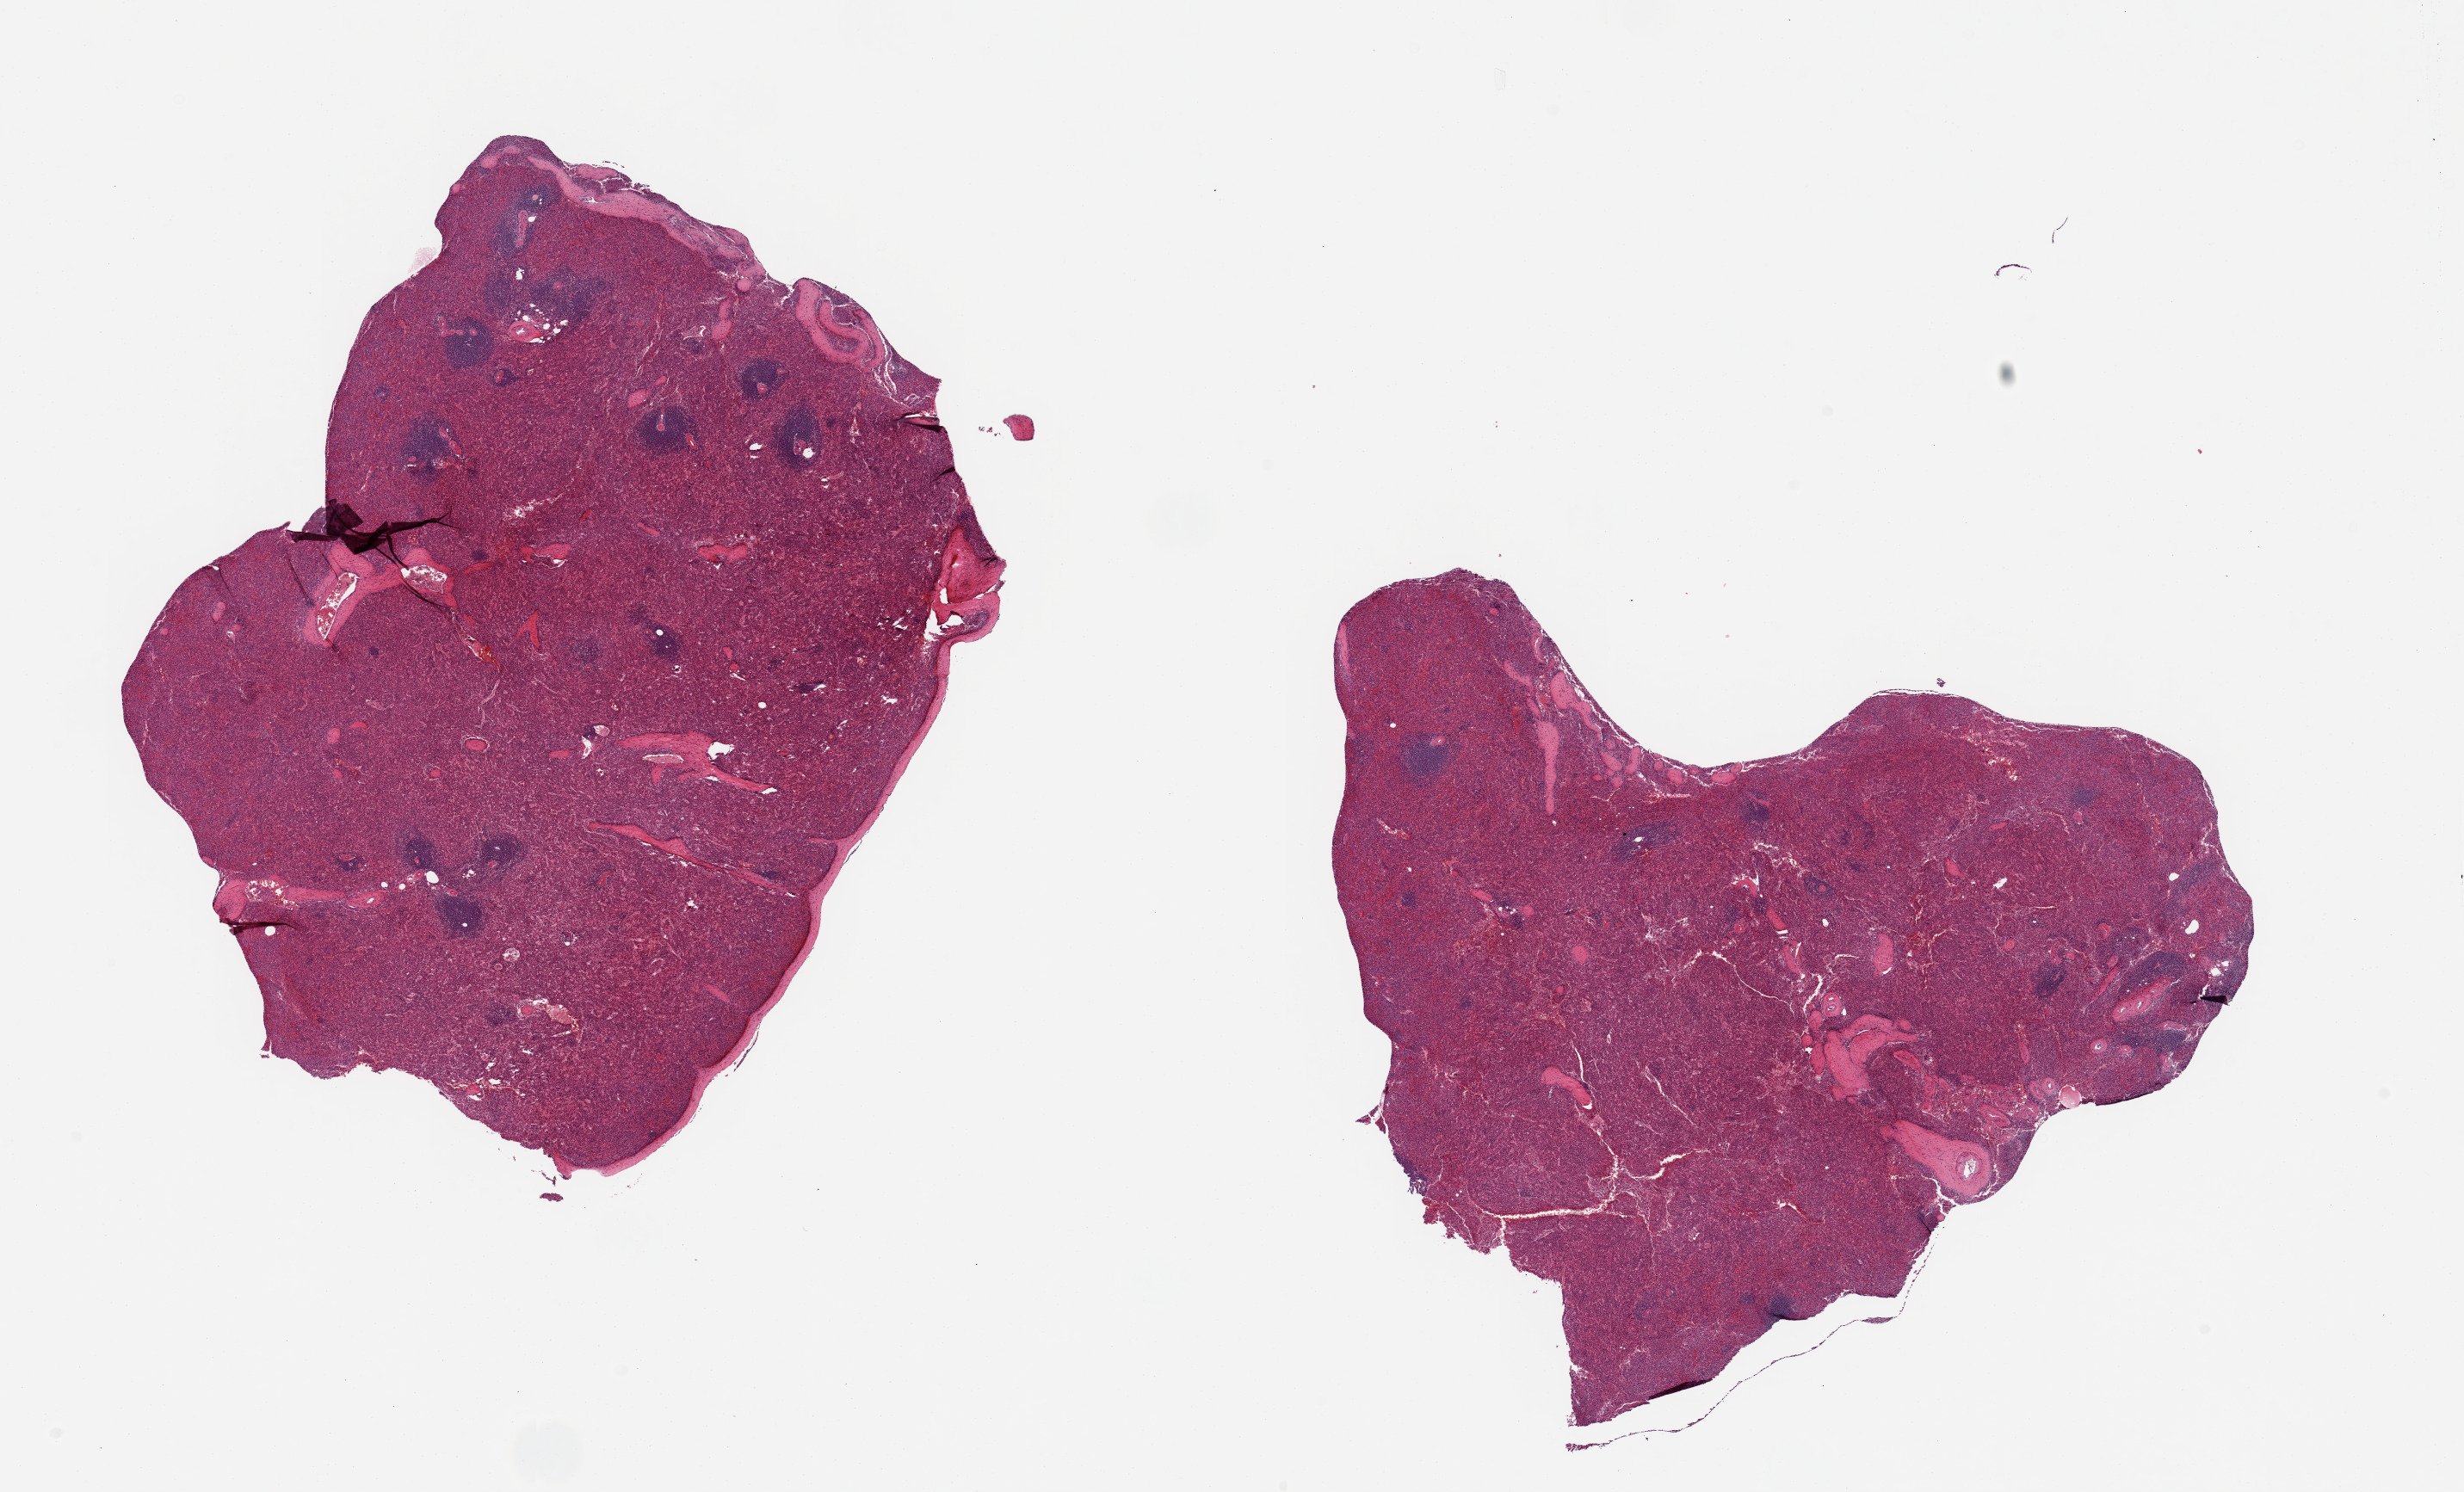
Haematoxylin and eosin whole-slide image — whole scanned area (about 22.6 x 13.7 mm, from a 20x scan) shown as a low-resolution overview; PAXgene-fixed, paraffin-embedded tissue; target tissue: spleen; donor tissue sample. Donor sex: male.
Reviewer comment on this tissue sample: 2 pieces ~8x7mm, Reasonably well-preserved.